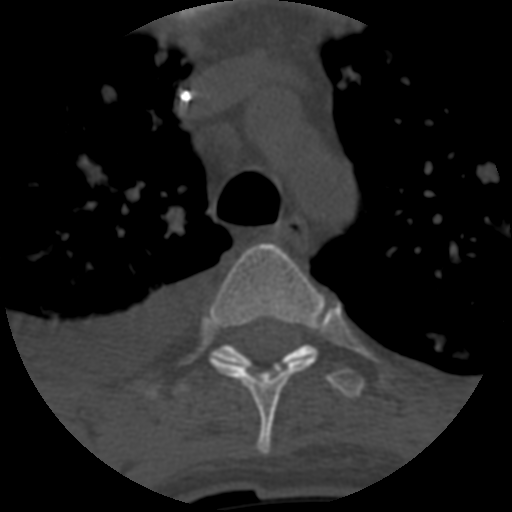
CT including the spine, one axial slice. Slice 465 of 708 in the series (ordered by position). One of 3 acquisitions stored at this slice position. Bone window (W 1800 / L 400 HU). 512 × 512 image matrix, field of view 160 × 160 mm. Patient age 55 years. Case-level facts recorded for this patient, not image findings: primary cancer: colon; vertebrae with lytic lesions (as recorded): T12, L1, L5.
Annotated regions visible in this slice (semi-automatic segmentation, software-assisted and operator-edited):
- T4 vertebra: bounding box <211,243,325,455> (left, top, right, bottom; pixels)
- T5 vertebra: <175,344,365,399>